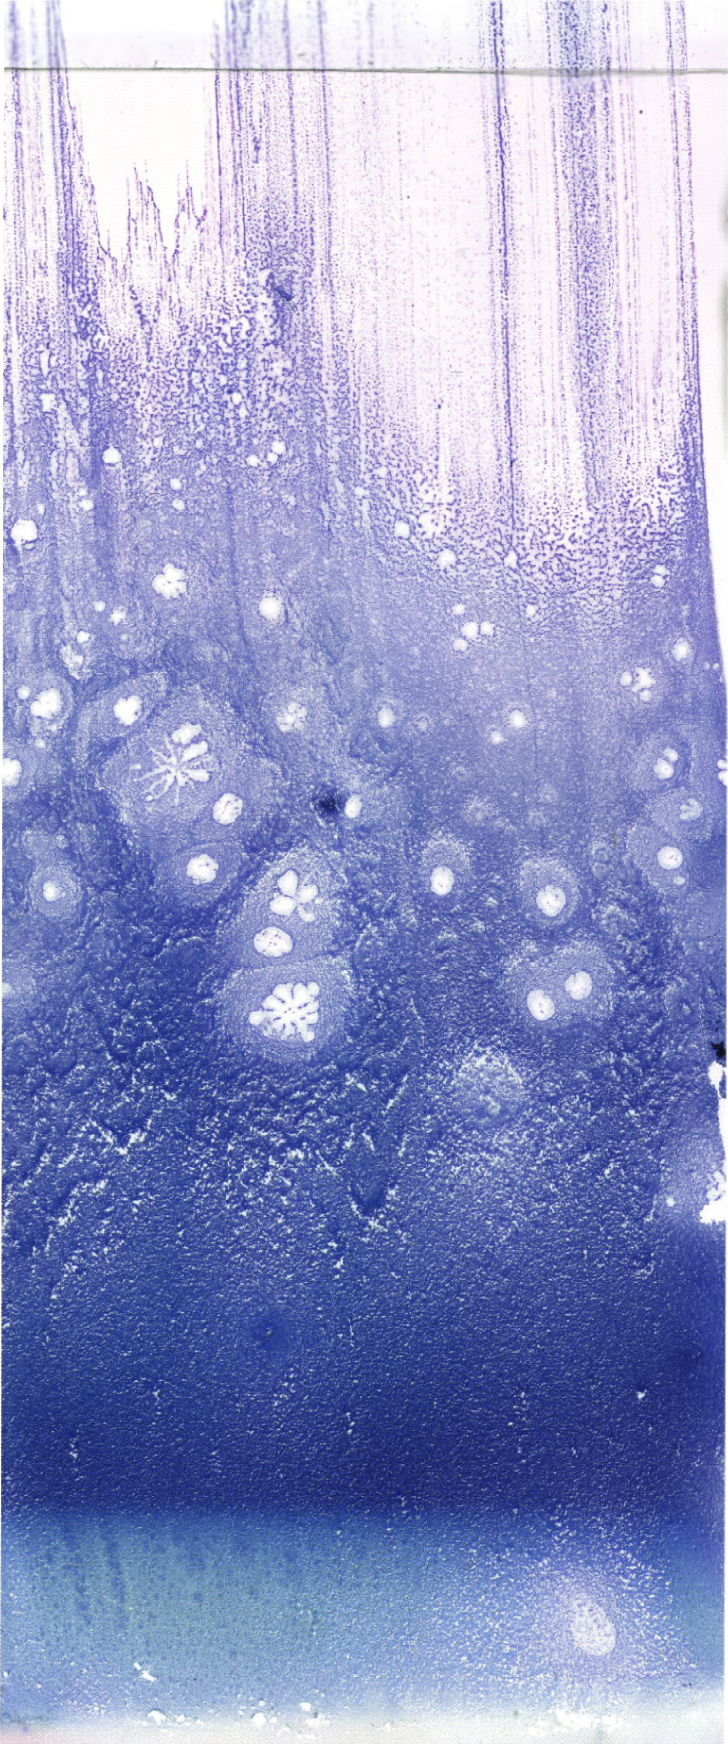
May-Grünwald–Giemsa-stained marrow aspirate smear (whole slide) — whole scanned area (about 20.6 x 49.4 mm) shown as a low-resolution overview. Patient sex: male.
Diagnosis: B Acute Lymphoblastic Leukemia.